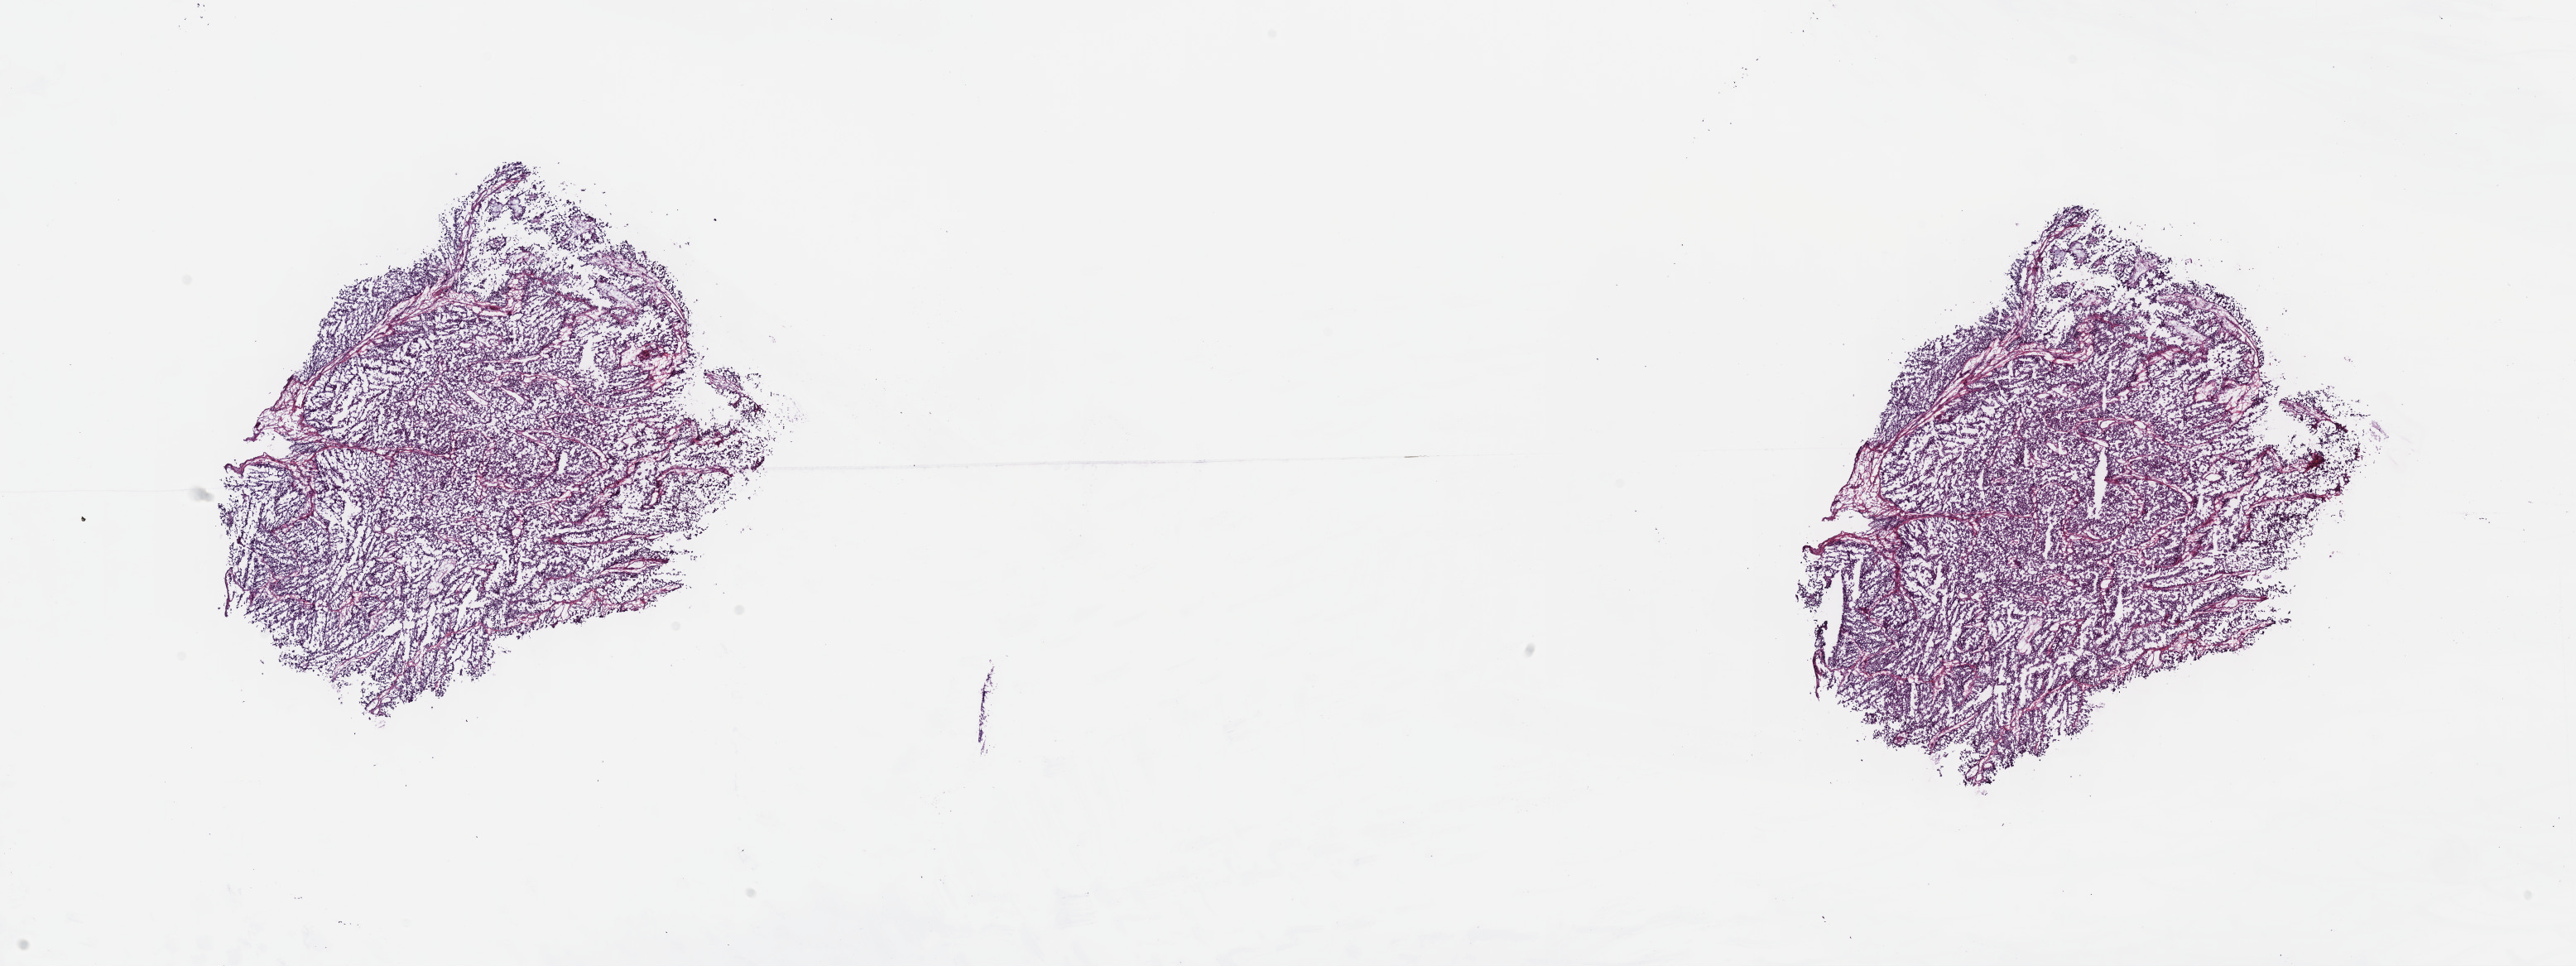
Whole-slide histology image, H&E — whole scanned area (about 25.2 x 9.4 mm, from a 40x scan) shown as a low-resolution overview; frozen section from the top of the tissue portion; sample: primary tumour, kidney. Male patient; age at initial diagnosis 75 years. Slide review estimates, as recorded: tumour cells 80%, tumour nuclei 95%, normal cells 0%, stromal cells 18%, necrosis 2%. Infiltration values recorded for this section: lymphocyte infiltration 3%, monocyte infiltration 0%, neutrophil infiltration 1%.
• pathologic diagnosis: Papillary adenocarcinoma, NOS
• AJCC pathologic stage: I (6th edition)